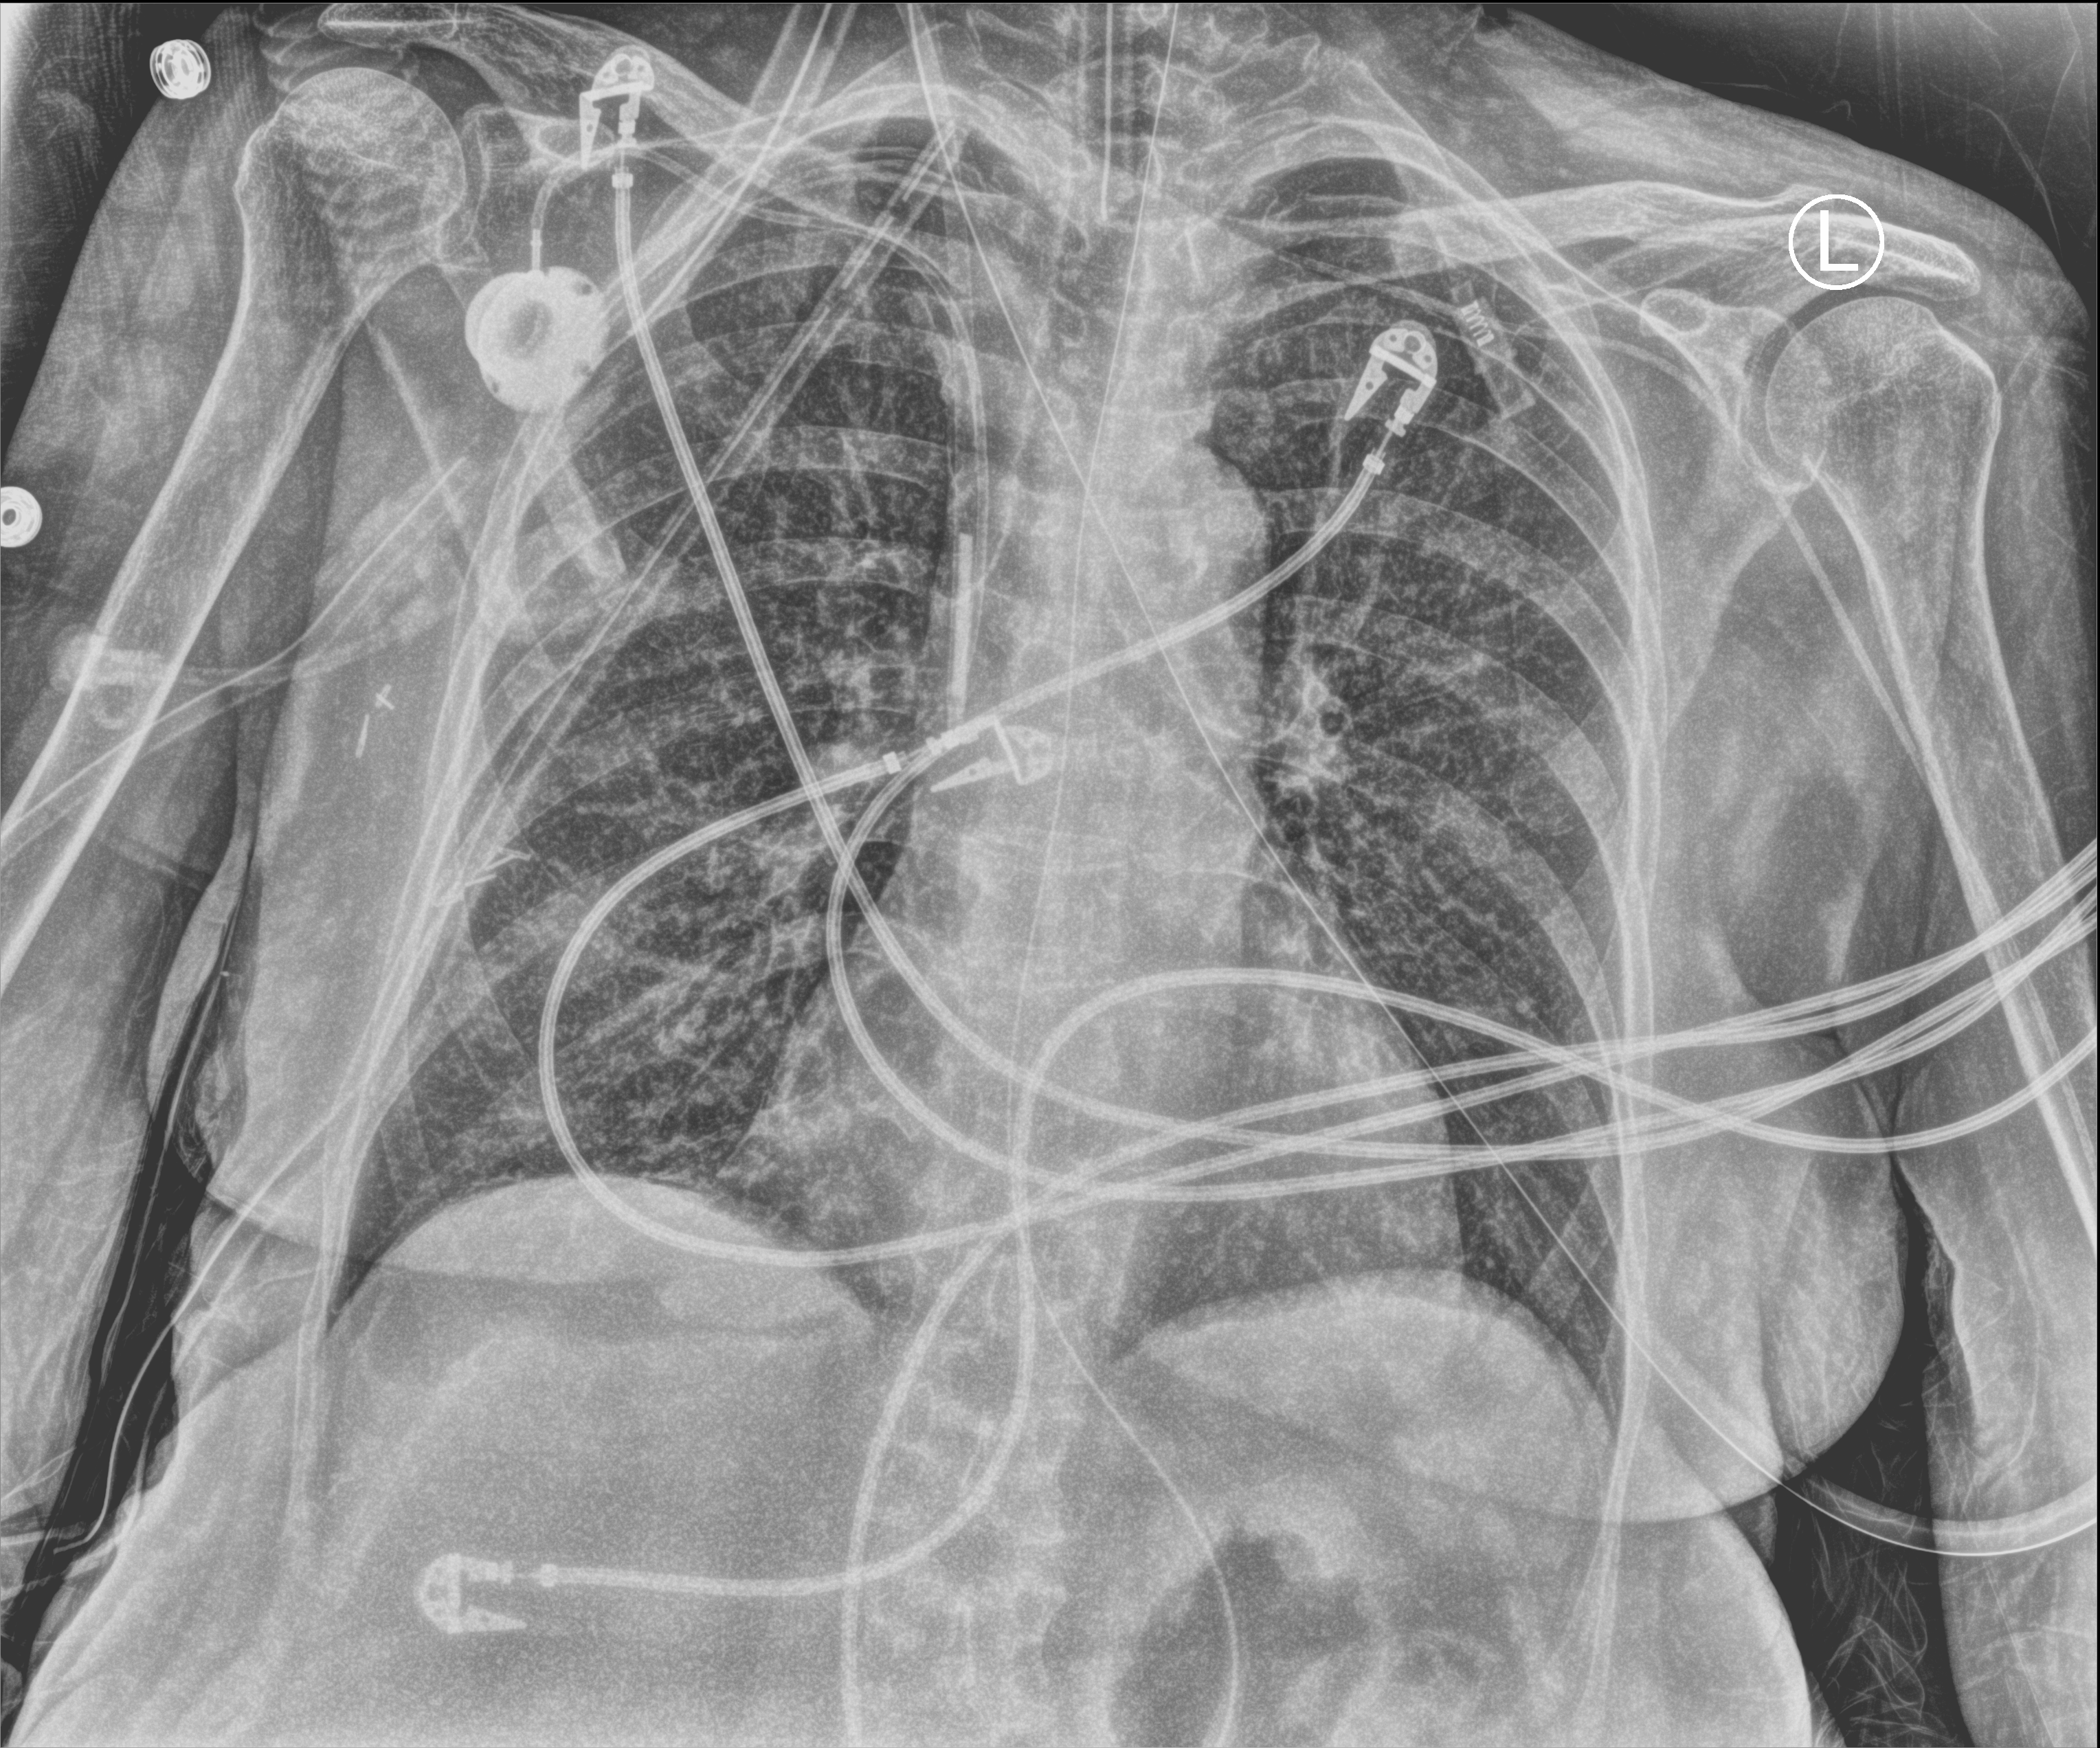
Portable chest radiograph, anteroposterior (AP) projection. Female patient hospitalised with COVID-19, age 60–74 years.
Hospital-stay facts (about this admission, not read from this image; timing relative to this image not recorded):
- length of hospital stay: 43 days